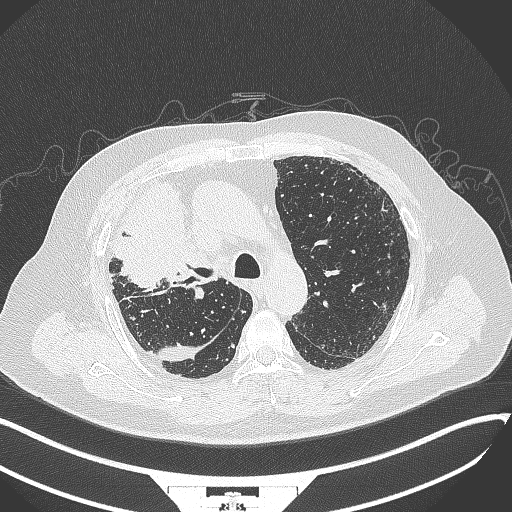
Chest CT, one axial slice; position 248 of 384 along the scan axis; reconstruction kernel B70f; lung window (W 1500 / L -600 HU); 1 mm slice thickness; 512 × 512 image matrix, field of view 400 × 400 mm. Patient: male, 69 years. Case-level facts recorded for this patient, not image findings: clinical TNM (as recorded): T4 N3 M1.
Outlined on this slice (rectangle marked by the reading radiologist):
- lung tumour (recorded histology: adenocarcinoma): bounding box [x1, y1, x2, y2] px = [105, 173, 200, 289]